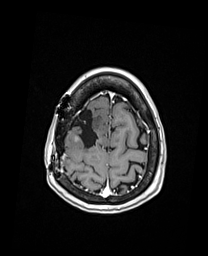
Brain MRI from a brain-tumour surgery series, one axial slice. Slice 37 of 192 in the series (ordered by position). T1-weighted post-contrast. 1 mm slice thickness. 208 × 256 image matrix, field of view 208 × 256 mm. From the clinical record (not read from this slice): histopathology: Oligodendroglioma; WHO grade: 3; IDH mutation: yes; tumour location: Right Frontal.
Annotated regions visible in this slice (manually delineated by an expert):
- previous resection cavity: bounding box (x1, y1, x2, y2) in pixels: (72, 109, 99, 148)